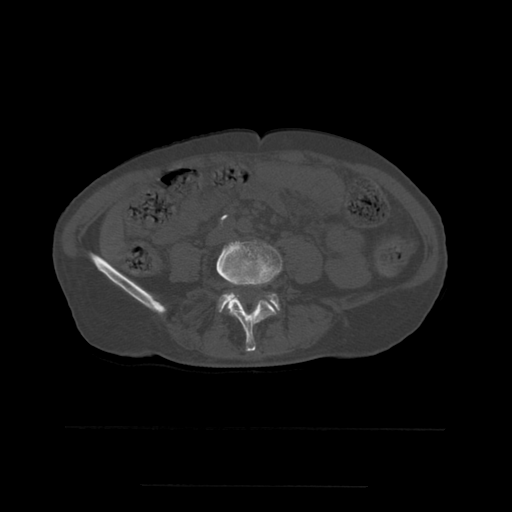
CT including the spine, one axial slice; slice 160 of 544 in the series (ordered by position); bone window (W 1800 / L 400 HU); 1.25 mm slice thickness; 512 × 512 image matrix, field of view 350 × 350 mm. Patient age 58 years. From the clinical record (not read from this slice): primary cancer: lung.
Annotated regions visible in this slice (semi-automatically segmented with operator editing):
- L4 vertebra: bounding box <216,242,283,352> (left, top, right, bottom; pixels)
- L5 vertebra: <219,293,280,312>